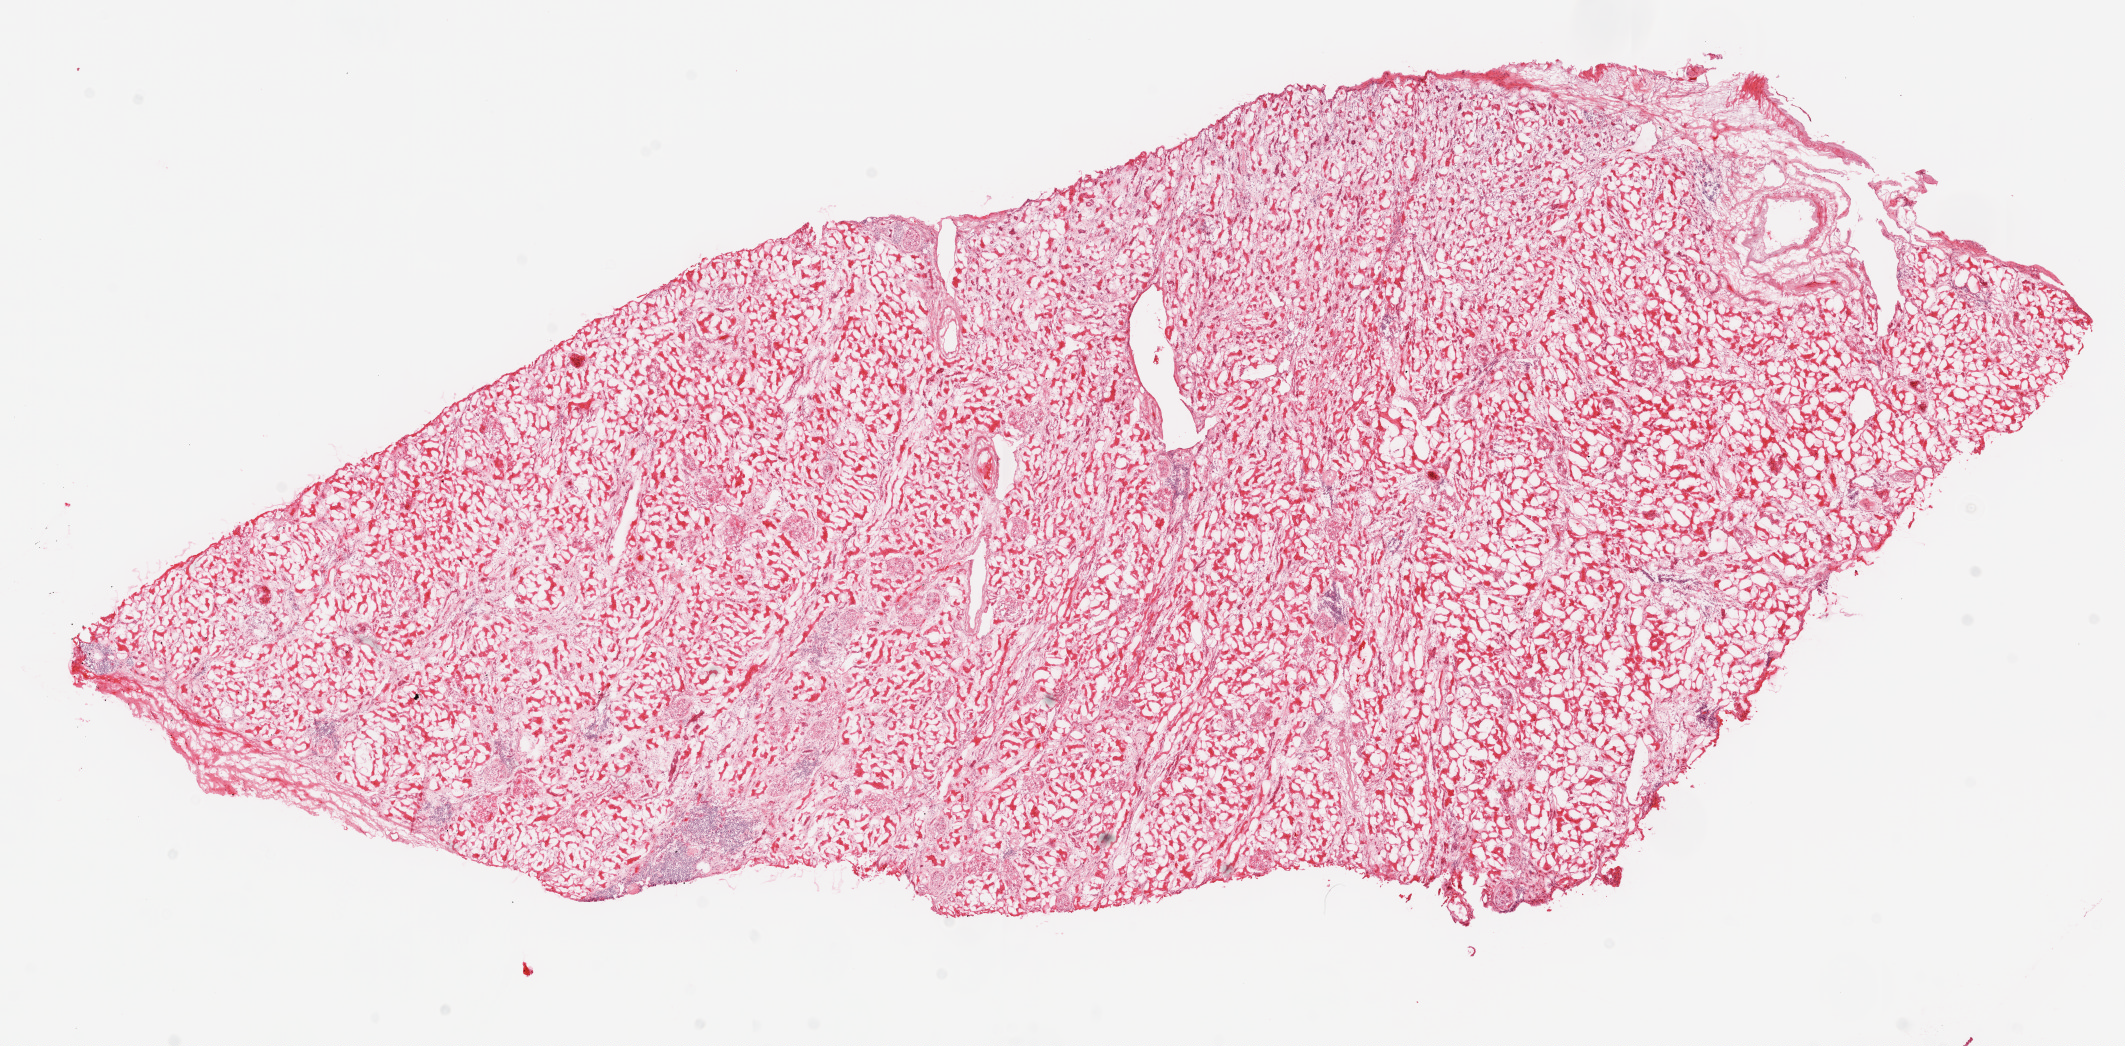
Whole-slide histology image, H&E-stained, shown as a low-resolution overview of the whole scanned area (about 17.1 x 8.4 mm, slide scanned at 20x), frozen section, kidney, solid tissue normal (non-tumour tissue) sample. Patient: male, age at initial diagnosis 63 years.
This section: solid tissue normal sample (biorepository sample class). Patient diagnosis: Clear cell adenocarcinoma, NOS.